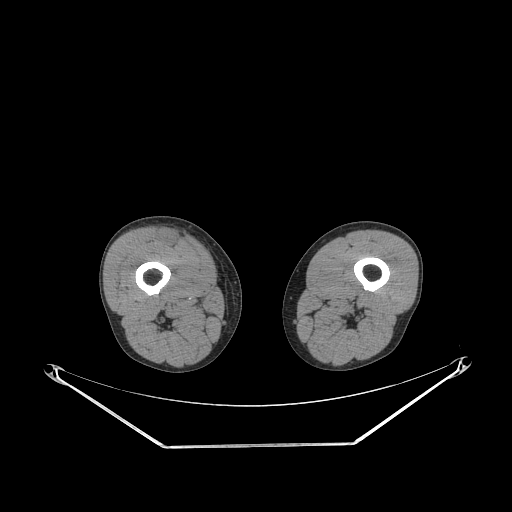
CT of an extremity soft-tissue mass (from a PET/CT study), one axial slice; position 229 of 311 along the scan axis; reconstruction kernel STANDARD; 140 kVp; soft-tissue window (W 400 / L 40 HU); 512 × 512 image matrix. Male patient. From the clinical record (not read from this slice): histological type: pleiomorphic leiomyosarcoma; grade: intermediate; site of the primary tumour: right thigh.
Annotated regions visible in this slice (expert contour drawn on MRI and transferred to this co-registered scan by the dataset authors):
- gross tumour volume including surrounding oedema: bounding box <158,228,184,247> (left, top, right, bottom; pixels)